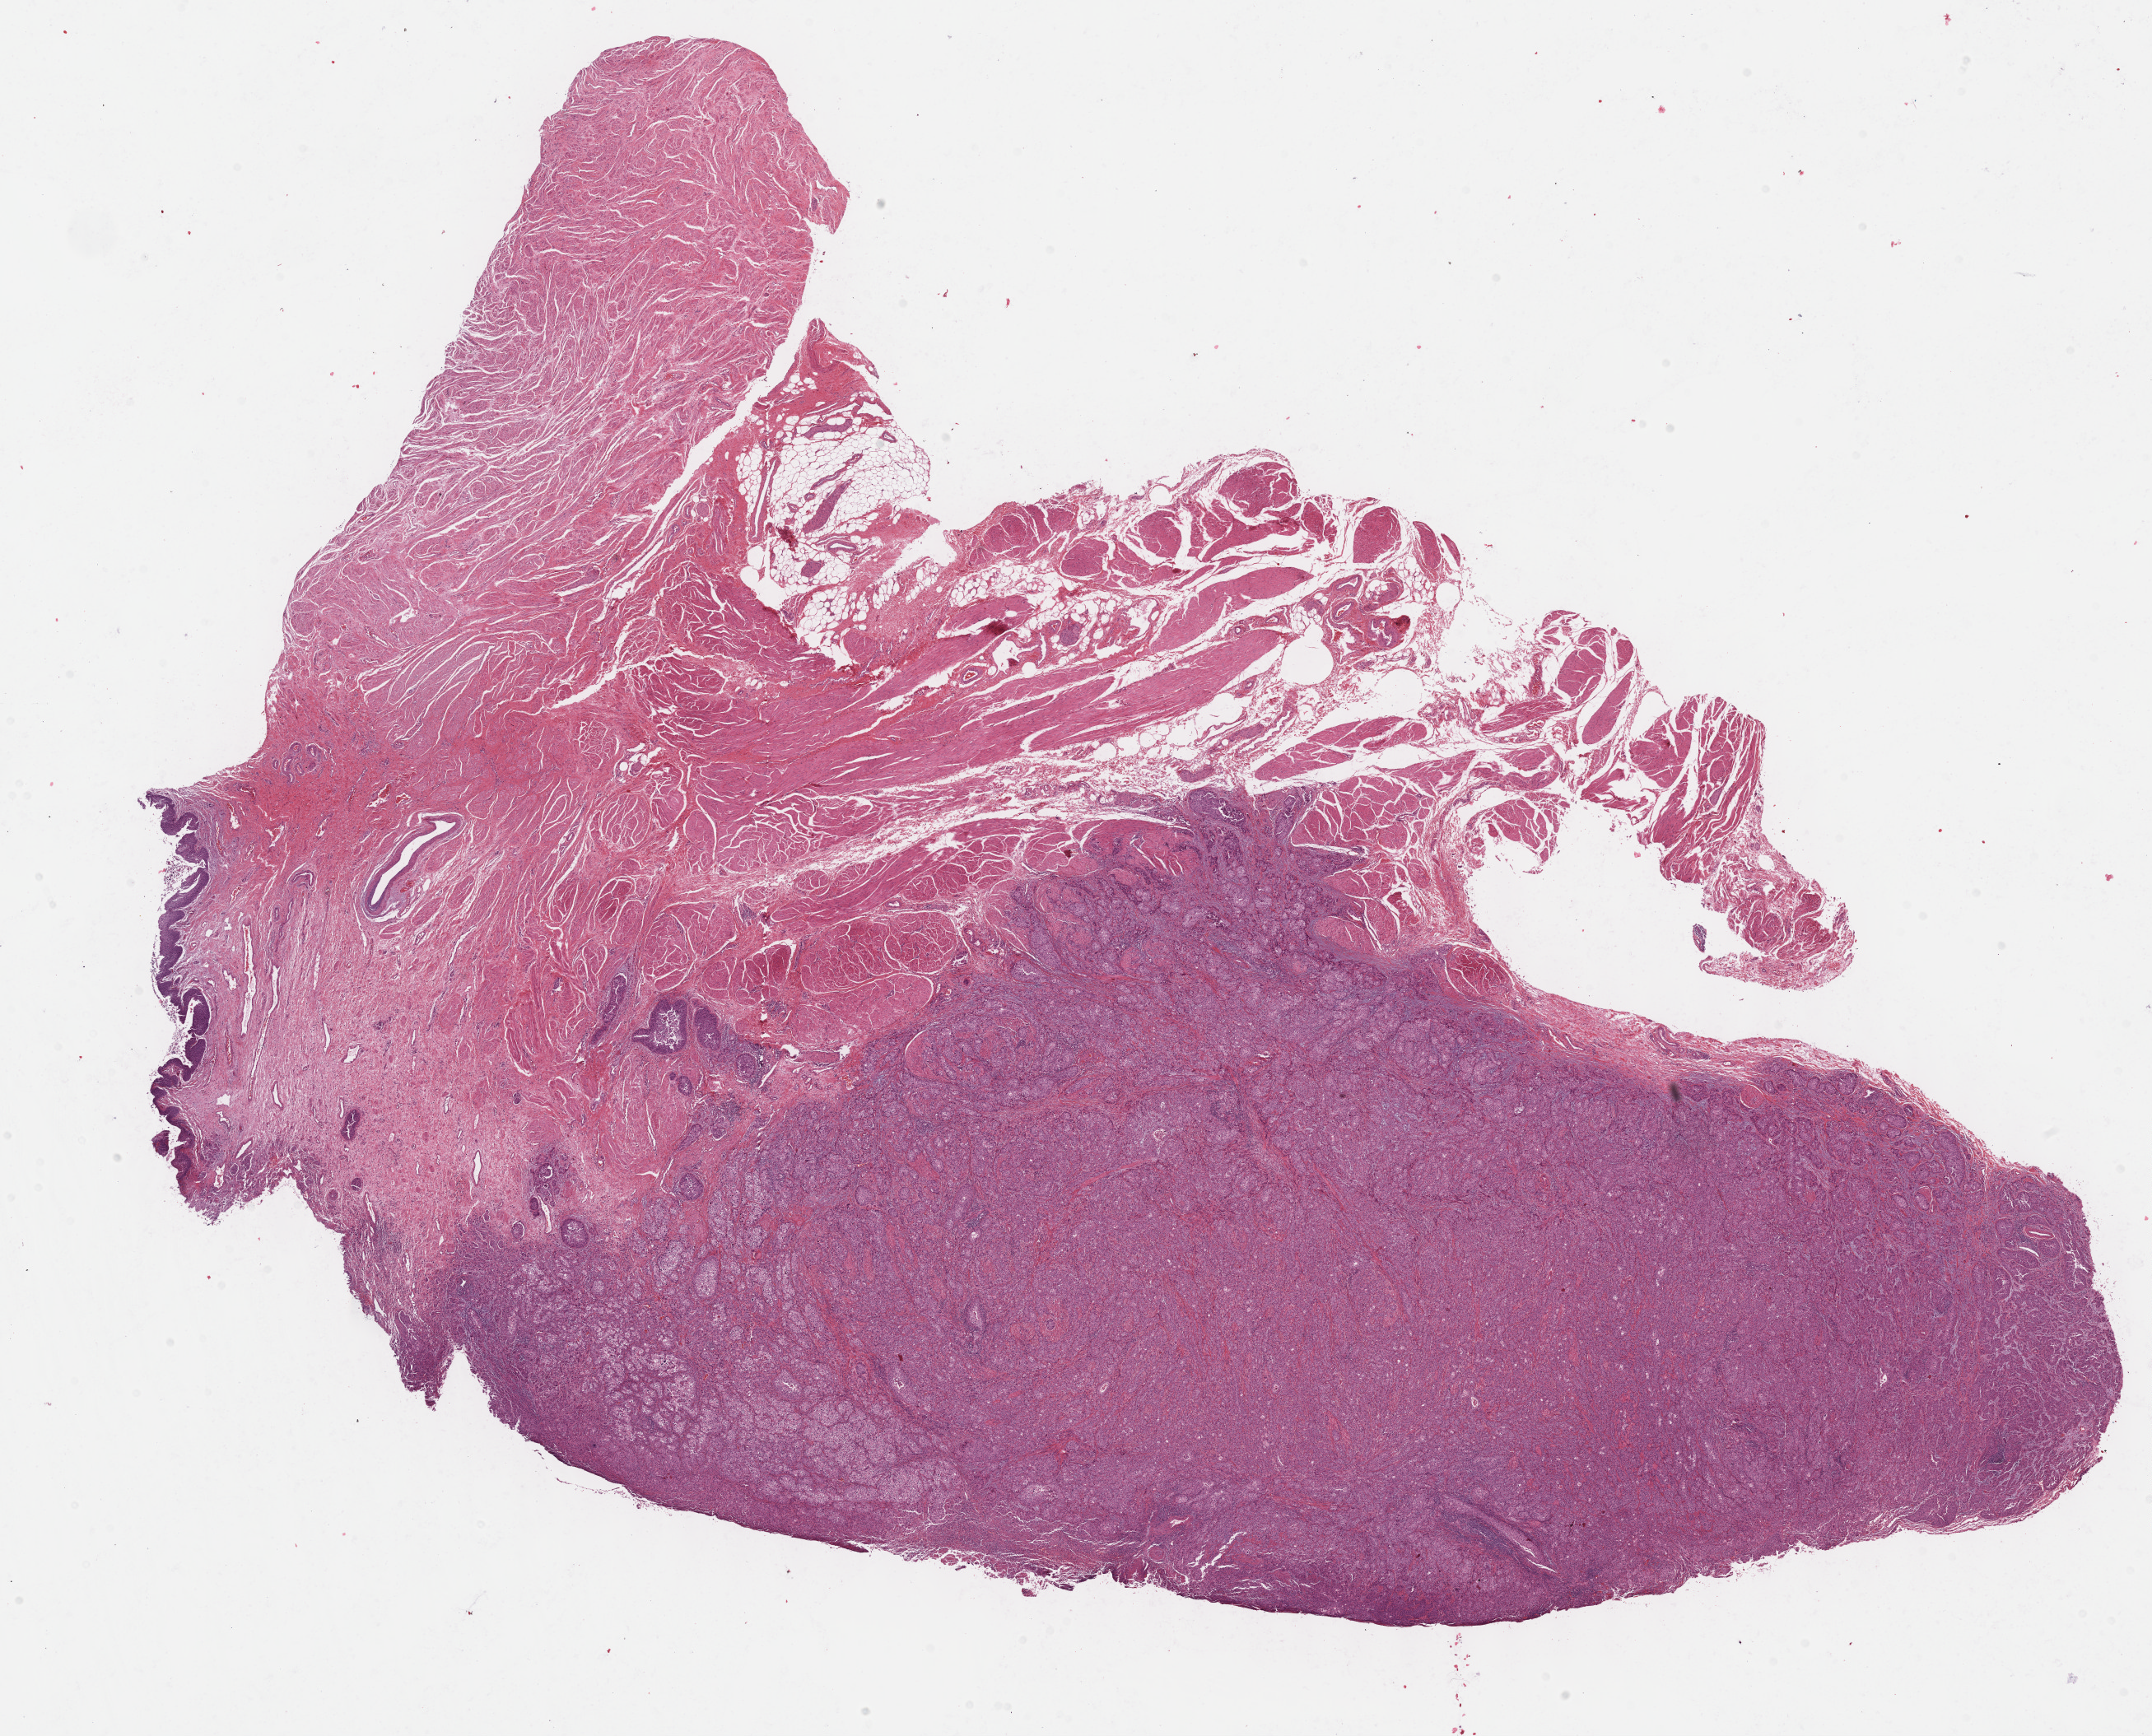
H&E whole-slide image, whole scanned area (about 21.1 x 17.1 mm) shown as a low-resolution overview; formalin-fixed paraffin-embedded (FFPE) diagnostic section; sample: primary tumour, bladder. Female patient; age at initial diagnosis 65 years. Histologic grade: high grade.
• TNM: T2b N0 M0
• lymph nodes positive (case pathology): 0 of 62 examined
• AJCC pathologic stage: II (6th edition)
• diagnosis: Transitional cell carcinoma